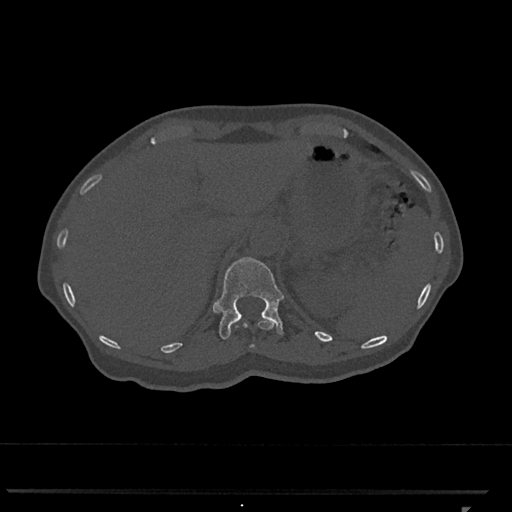
CT including the spine, one axial slice; position 480 of 793 along the scan axis; reconstruction kernel Br40s/3; bone window (W 1800 / L 400 HU); 512 × 512 image matrix, field of view 380 × 380 mm. Female patient, age 62 years. Case-level facts recorded for this patient, not image findings: primary cancer: renal.
Annotated regions visible in this slice (semi-automatic segmentation, software-assisted and operator-edited):
- T11 vertebra: bounding box <244,319,274,348> (left, top, right, bottom; pixels)
- T12 vertebra: <214,257,284,340>